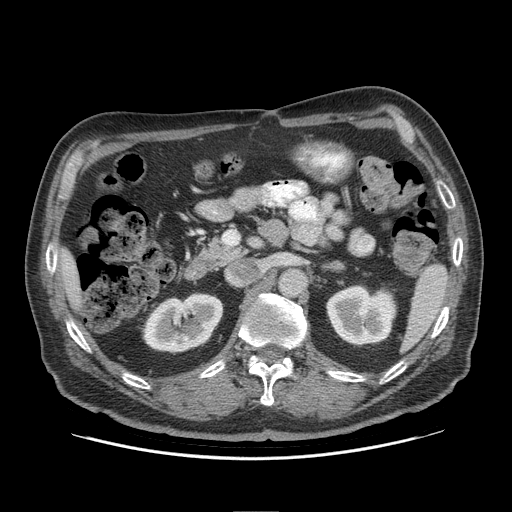
Contrast-enhanced abdominal CT (liver protocol), one axial slice; slice 45 of 95 in the series (ordered by position); soft-tissue window (W 400 / L 40 HU); 2.5 mm slice thickness; 512 × 512 image matrix, field of view 400 × 400 mm. From the clinical record (not read from this slice): diagnosis: hepatocellular carcinoma (patient treated with transarterial chemoembolisation; whether this scan precedes or follows treatment is not stated here); TNM stage (as recorded): Stage-IVB; Child-Pugh class: A; tumour nodularity: uninodular.
Outlined on this slice (semi-automatic segmentation, software-assisted and operator-edited):
- liver parenchyma outside the tumour (the mass and vessels are separate outlines, so this box may not span the whole liver): box from (x=58, y=248) to (x=82, y=311) px